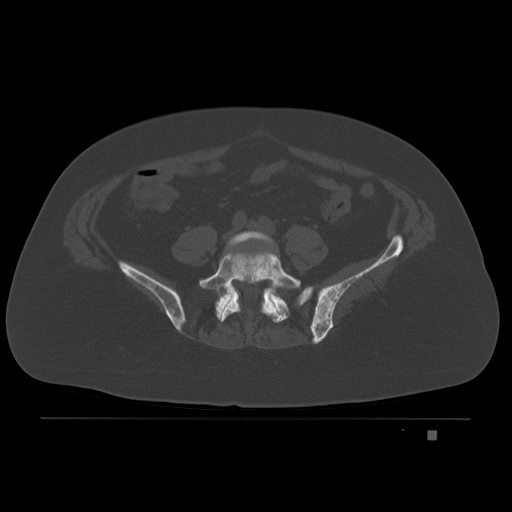
CT including the spine, one axial slice. Position 31 of 221 along the scan axis. Bone window (W 1800 / L 400 HU). 512 × 512 image matrix, field of view 474 × 474 mm. Patient: female, 63 years. From the clinical record (not read from this slice): primary cancer: breast.
Structures marked on this image (semi-automatic segmentation, software-assisted and operator-edited):
- L4 vertebra: box from (x=225, y=230) to (x=278, y=252) px
- L5 vertebra: (x=199, y=252)–(x=299, y=322)